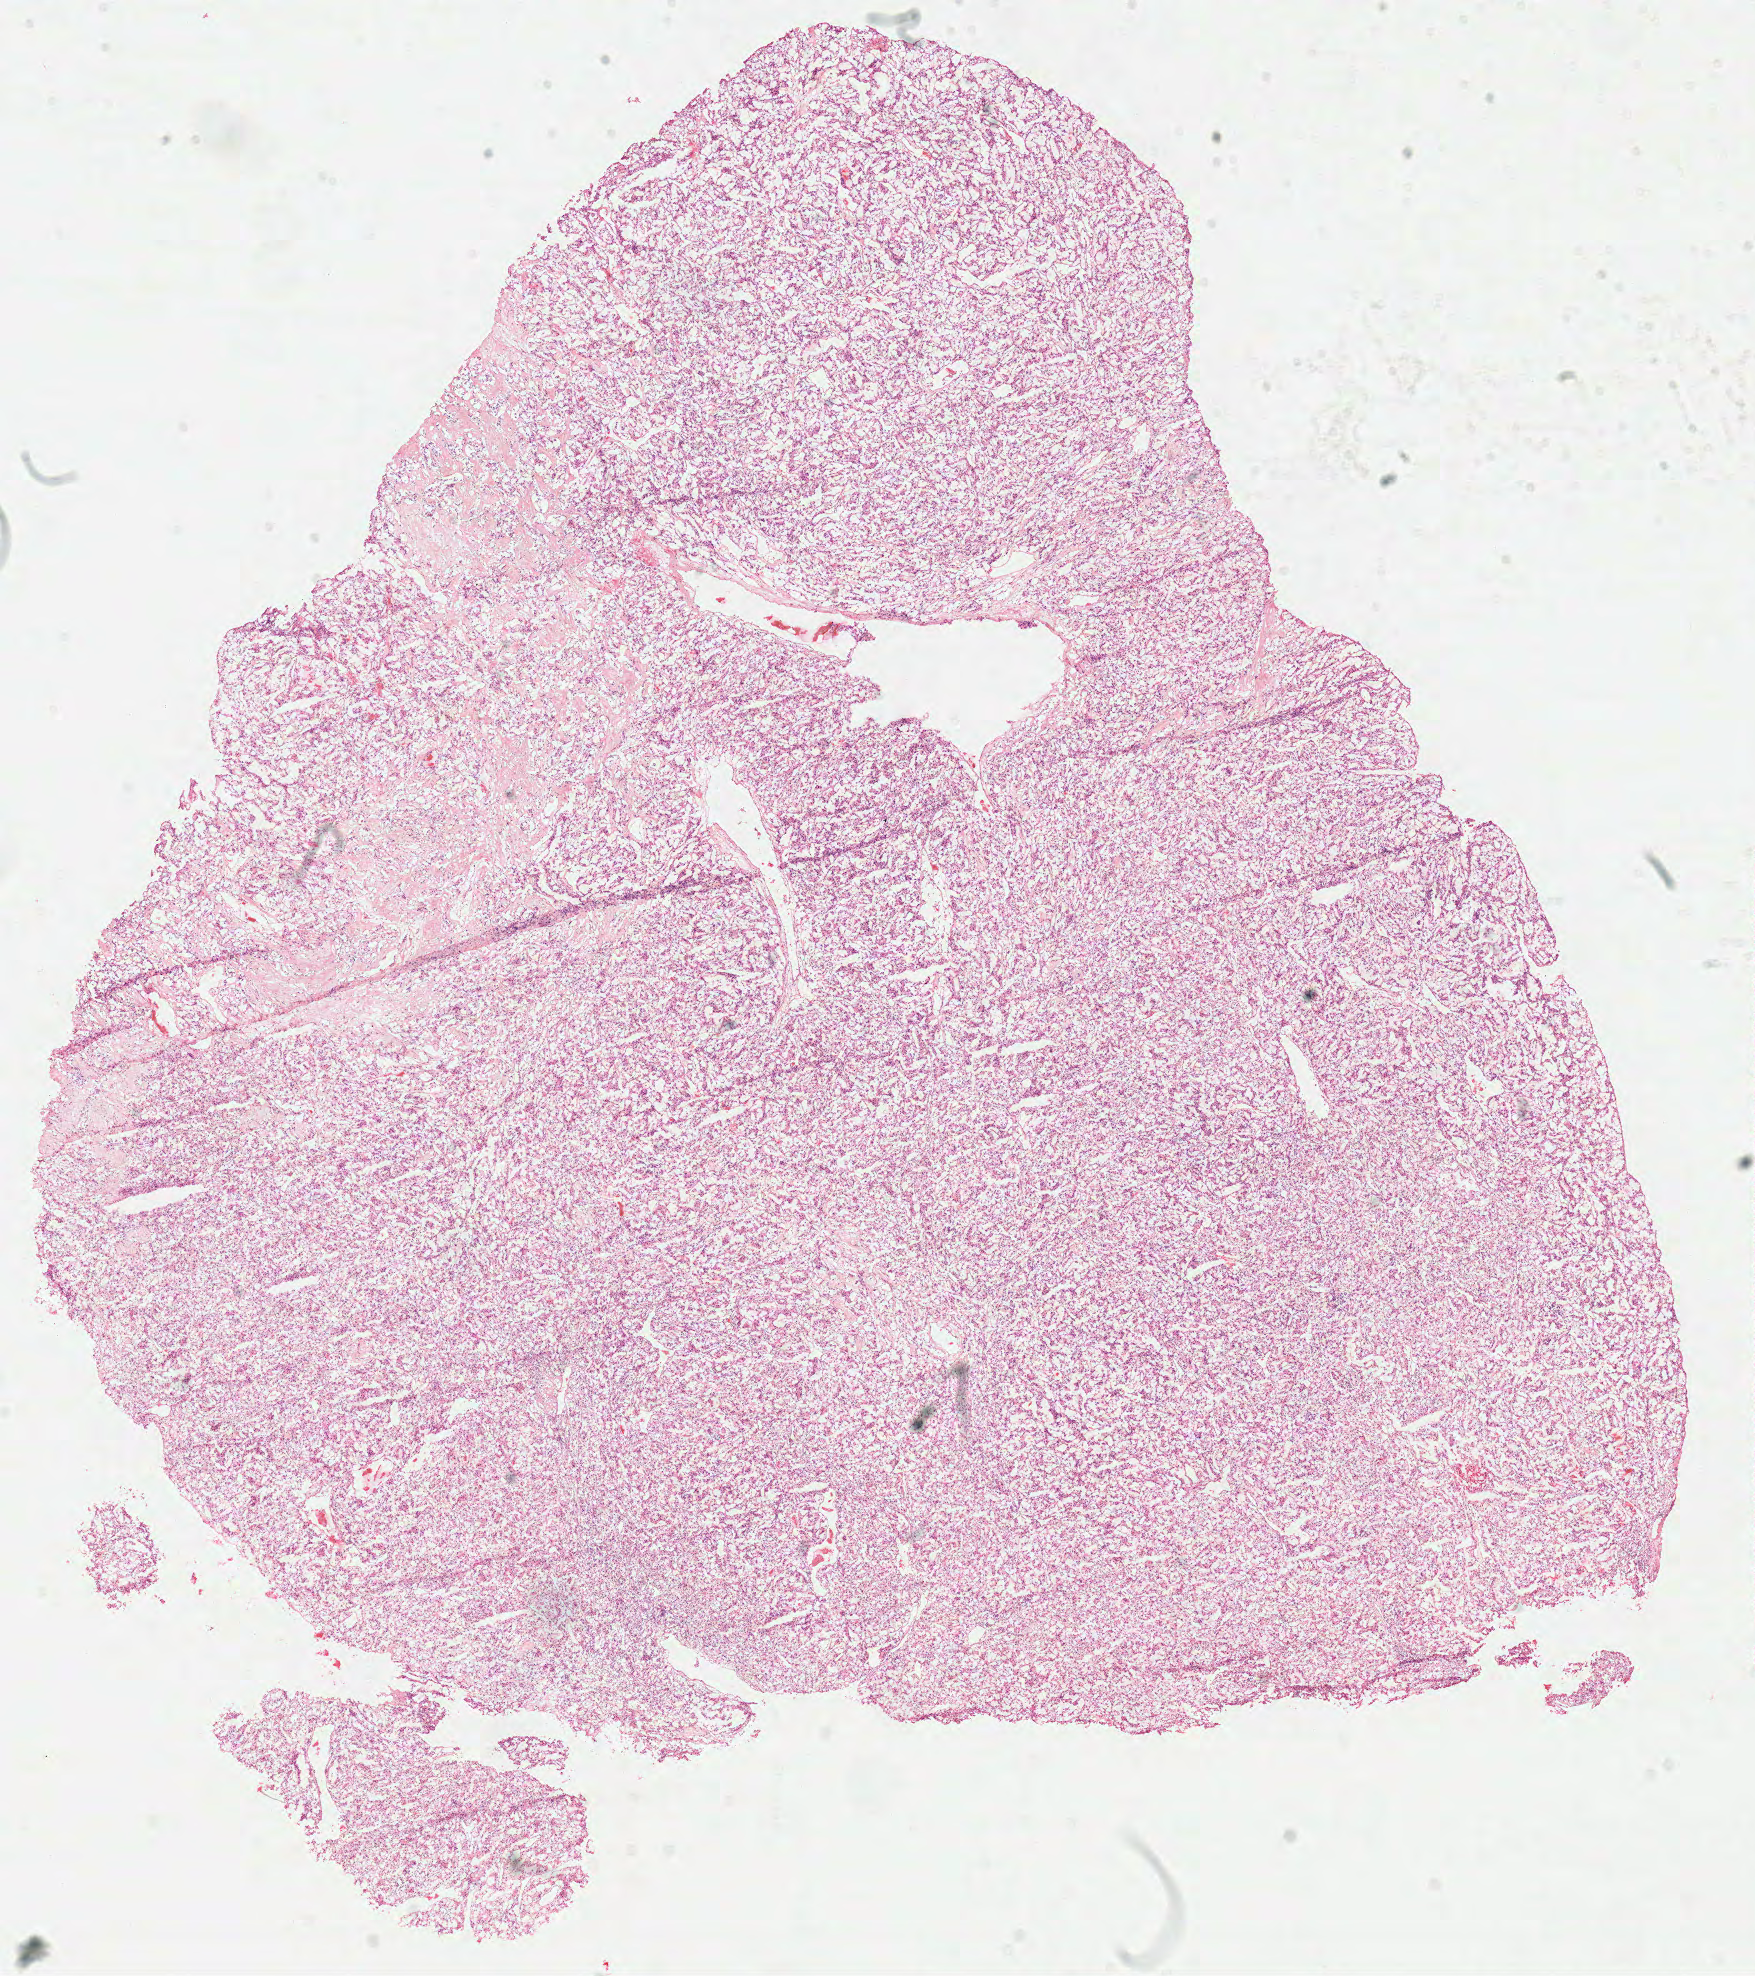
H&E-stained whole-slide image, whole scanned area (about 13.8 x 15.6 mm, acquisition: 40x scan) shown as a low-resolution overview; frozen section from the top of the tissue portion; primary tumour sample from the kidney. Patient: male, age at initial diagnosis 51 years. Histologic grade: G3 (poorly differentiated). Composition of this section per pathologist review: tumour cells 90%, tumour nuclei 80%, normal cells 0%, stromal cells 10%, necrosis 0%.
Pathologic diagnosis: Clear cell adenocarcinoma, NOS. AJCC pathologic stage: I (6th edition). TNM: T1b N0 M0.